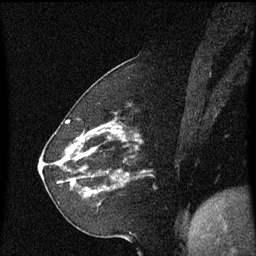
Breast MRI (dynamic contrast-enhanced), one sagittal slice. Slice 19 of 60 in the series (ordered by position). Dynamic contrast-enhanced series, image 2 of 3 at this slice position (ordered by acquisition). 1.5 T. TE 4.2 ms, TR 8.4 ms. 2.2 mm slice thickness. 256 × 256 image matrix, field of view 200 × 200 mm. Patient: female, 60 years. From the clinical record (not read from this slice): setting: breast cancer imaged before/during neoadjuvant chemotherapy; receptor status: triple-negative.
Annotated regions visible in this slice (semi-automatic segmentation, software-assisted and operator-edited):
- analysis volume of interest (the breast-tissue region the enhancement analysis was run in; not a lesion): bounding box <68,142,145,207> (left, top, right, bottom; pixels)
- tumour enhancement mask (voxels above the 70 % enhancement threshold inside the analysis volume of interest): <80,154,96,193>